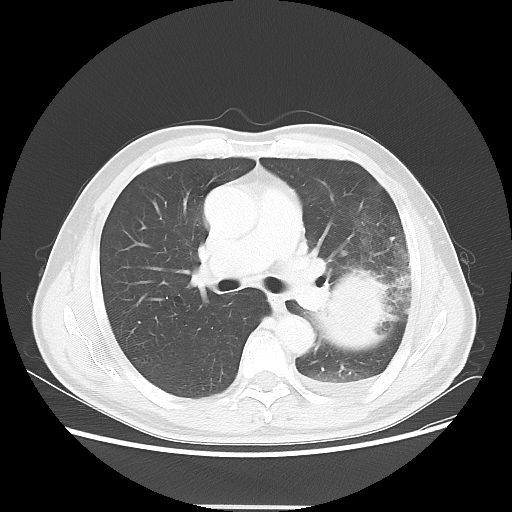
Chest CT, one axial slice; slice 32 of 53 in the series (ordered by position); reconstruction kernel LUNG; 100 kVp; lung window (W 1500 / L -600 HU); 5 mm slice thickness; 512 × 512 image matrix. Patient: male, 60 years. From the clinical record (not read from this slice): clinical TNM (as recorded): T4 N1 M1a; histopathological grade: G3.
Outlined on this slice (bounding box drawn by a radiologist):
- lung tumour (recorded histology: large cell carcinoma): bounding box <302,248,411,365> (left, top, right, bottom; pixels)